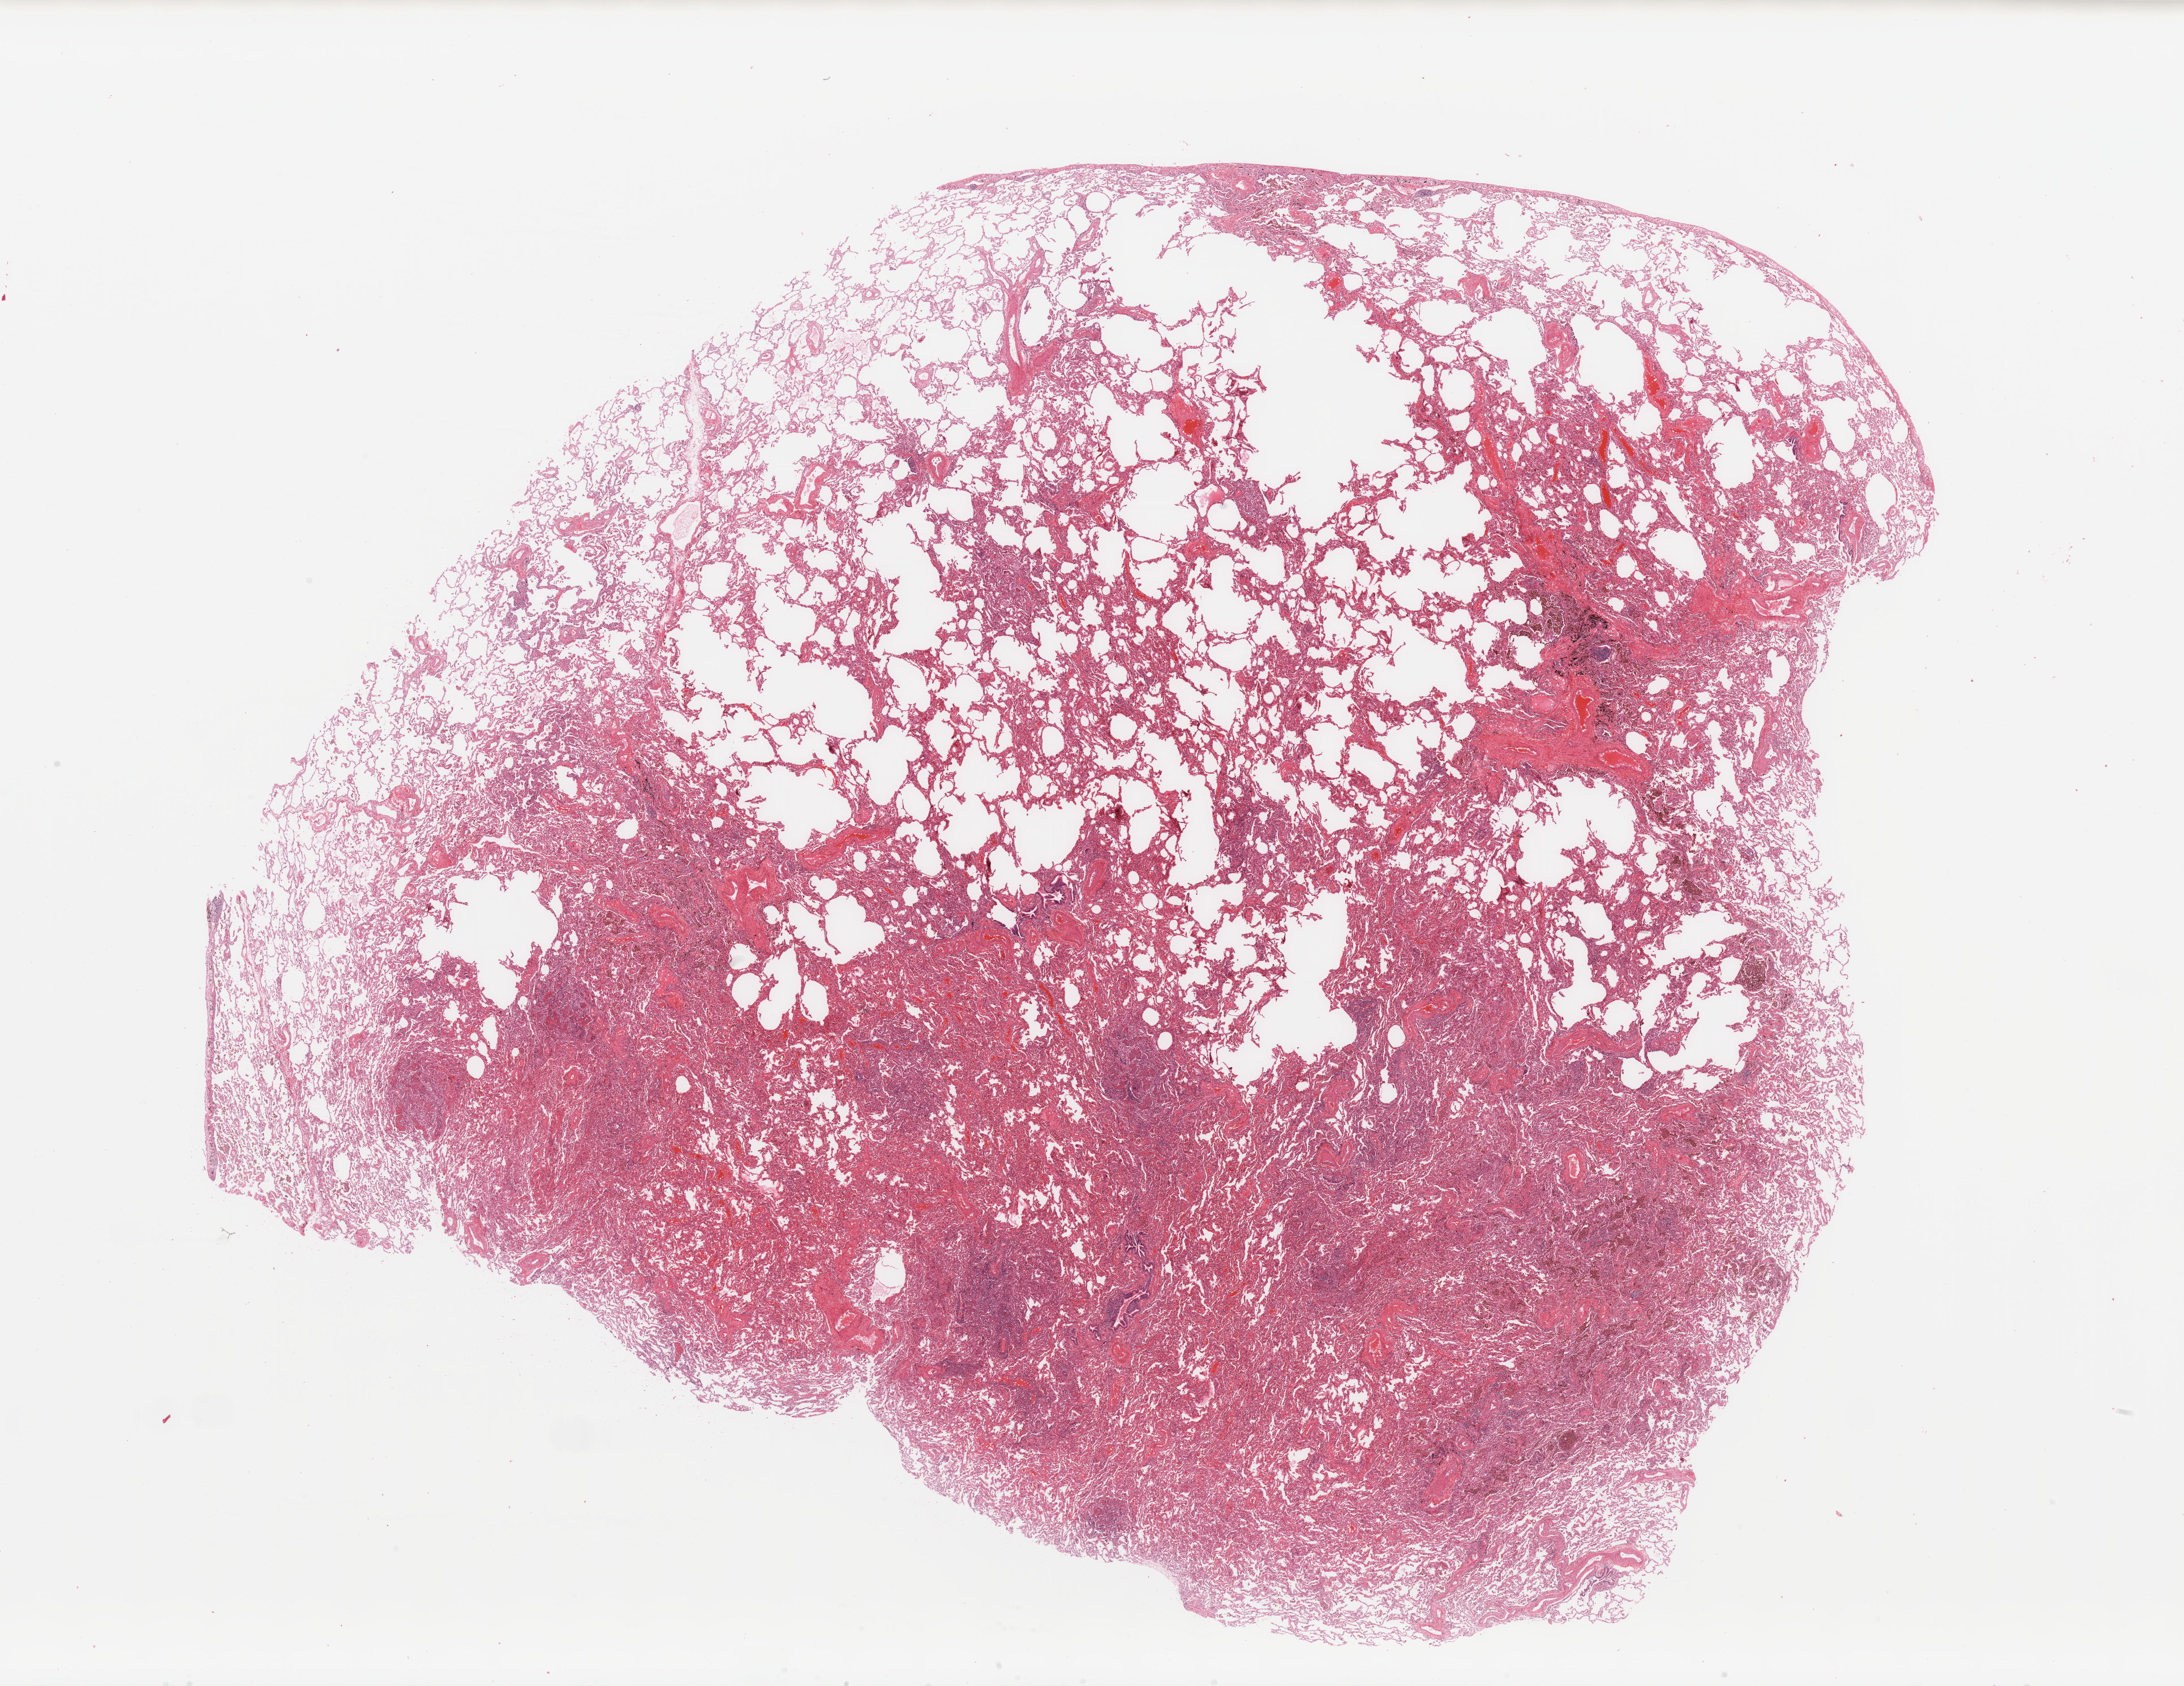
Whole-slide histology image, H&E-stained, low-resolution overview of the scanned area, about 30.5 x 23.6 mm; normal (non-tumour) tissue sample, sampled site: lung. Male, 58 y/o.
- this section: normal (non-tumour) tissue from the same patient
- patient diagnosis: Adenocarcinoma, NOS